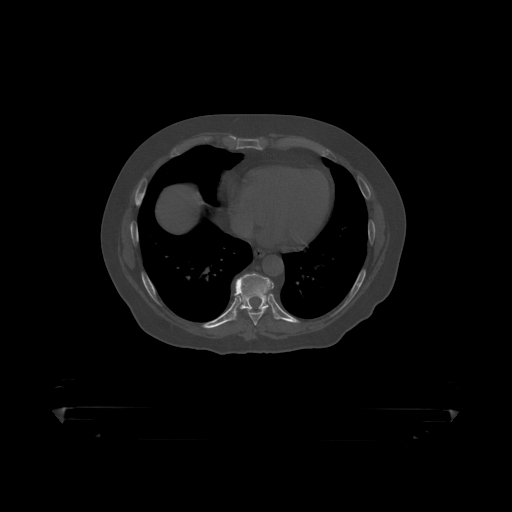
CT including the spine, one axial slice; slice 247 of 390 in the series (ordered by position); reconstruction kernel STANDARD; 120 kVp; bone window (W 1800 / L 400 HU); 1.25 mm slice thickness; 512 × 512 image matrix, field of view 650 × 650 mm. Patient: male, 60 years. Case-level facts recorded for this patient, not image findings: primary cancer: prostate.
Annotated regions visible in this slice (semi-automatic segmentation, software-assisted and operator-edited):
- T8 vertebra: bounding box (x1, y1, x2, y2) in pixels: (249, 284, 275, 319)
- T9 vertebra: (233, 274, 273, 316)